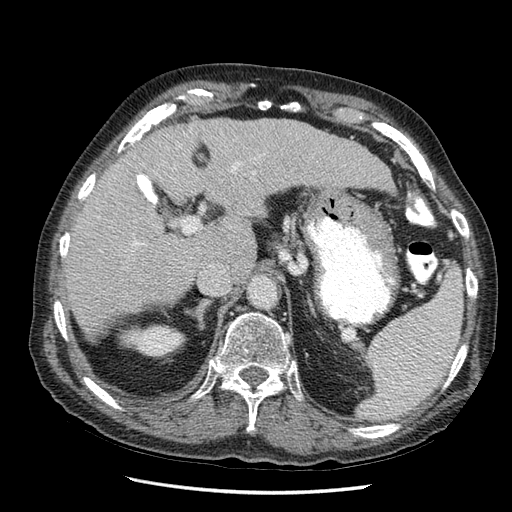
Contrast-enhanced abdominal CT (liver protocol), one axial slice. Slice 30 of 67 in the series (ordered by position). 120 kVp. Soft-tissue window (W 400 / L 40 HU). 2.5 mm slice thickness. 512 × 512 image matrix, field of view 360 × 360 mm. From the clinical record (not read from this slice): diagnosis: hepatocellular carcinoma (patient treated with transarterial chemoembolisation; whether this scan precedes or follows treatment is not stated here); TNM stage (as recorded): Stage-I.
Annotated regions visible in this slice (semi-automatically segmented with operator editing):
- liver parenchyma outside the tumour (the mass and vessels are separate outlines, so this box may not span the whole liver): bounding box (x1, y1, x2, y2) in pixels: (63, 116, 395, 350)
- liver vessels: (100, 152, 267, 244)